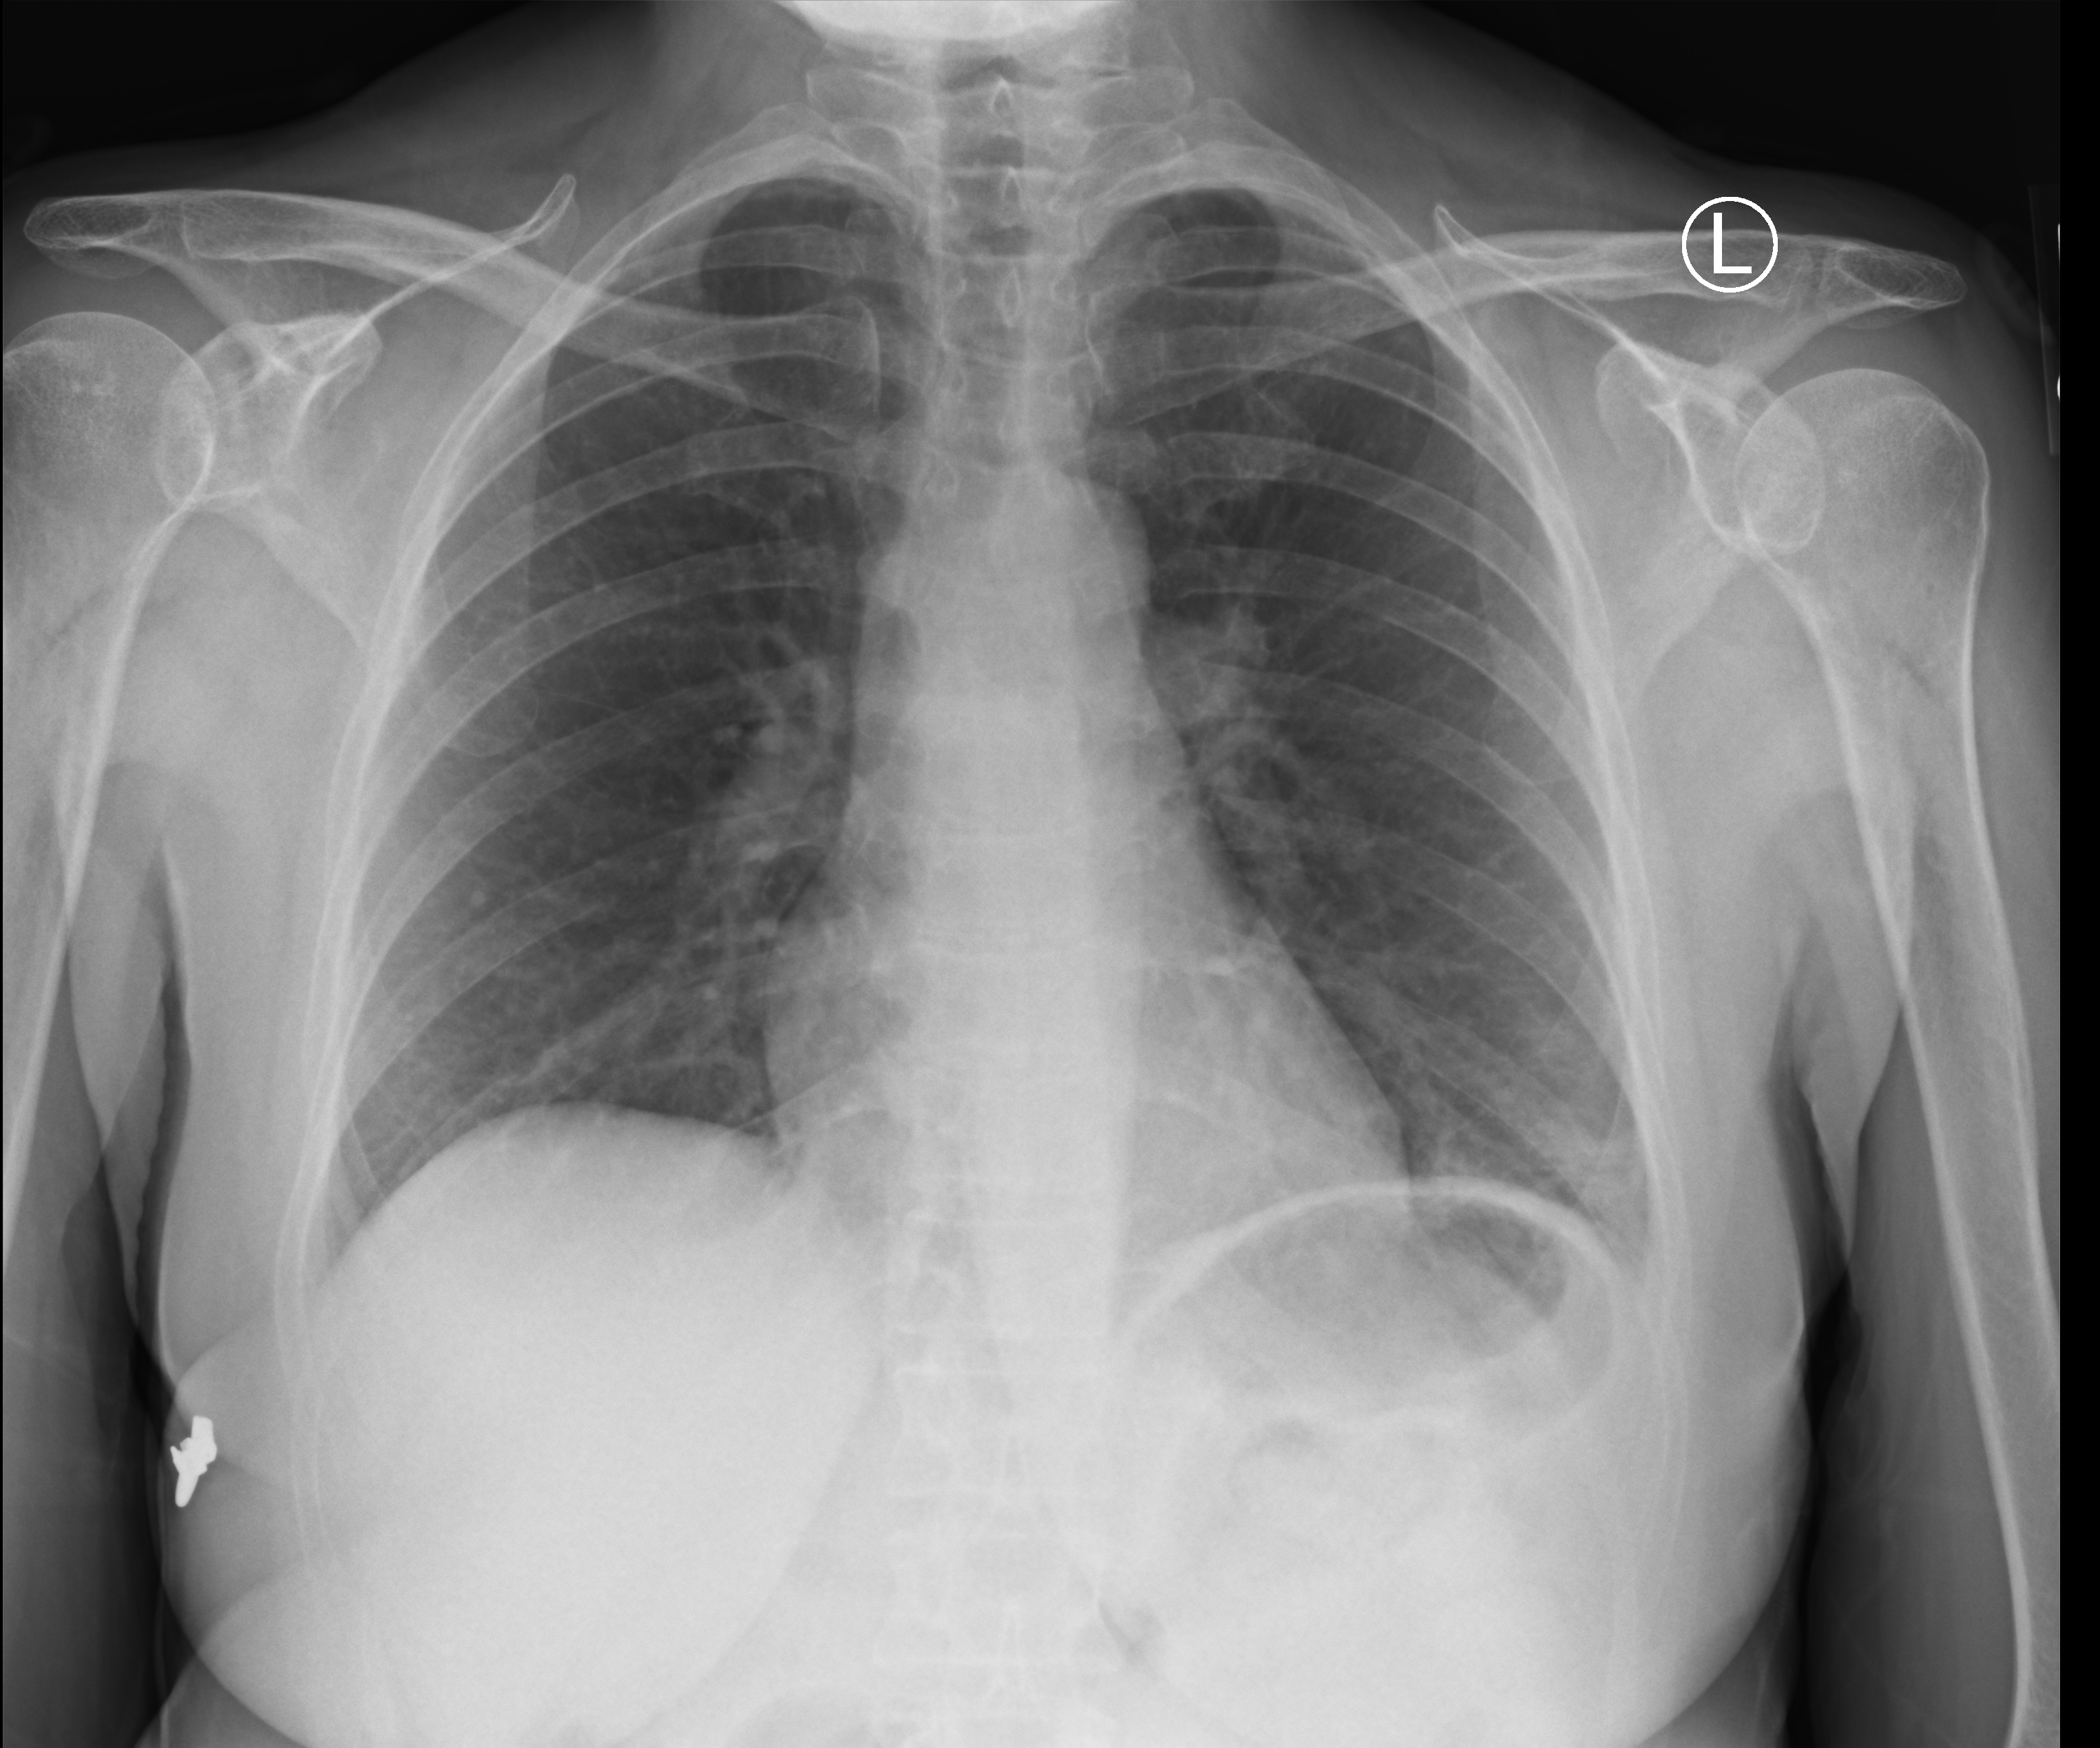
Portable chest radiograph, anteroposterior (AP) projection. Patient hospitalised with COVID-19; female, aged 18–59 years.
From the hospital-stay record, not from the radiograph (when in the stay this image was taken is not recorded):
- mechanically ventilated during this hospital stay: no